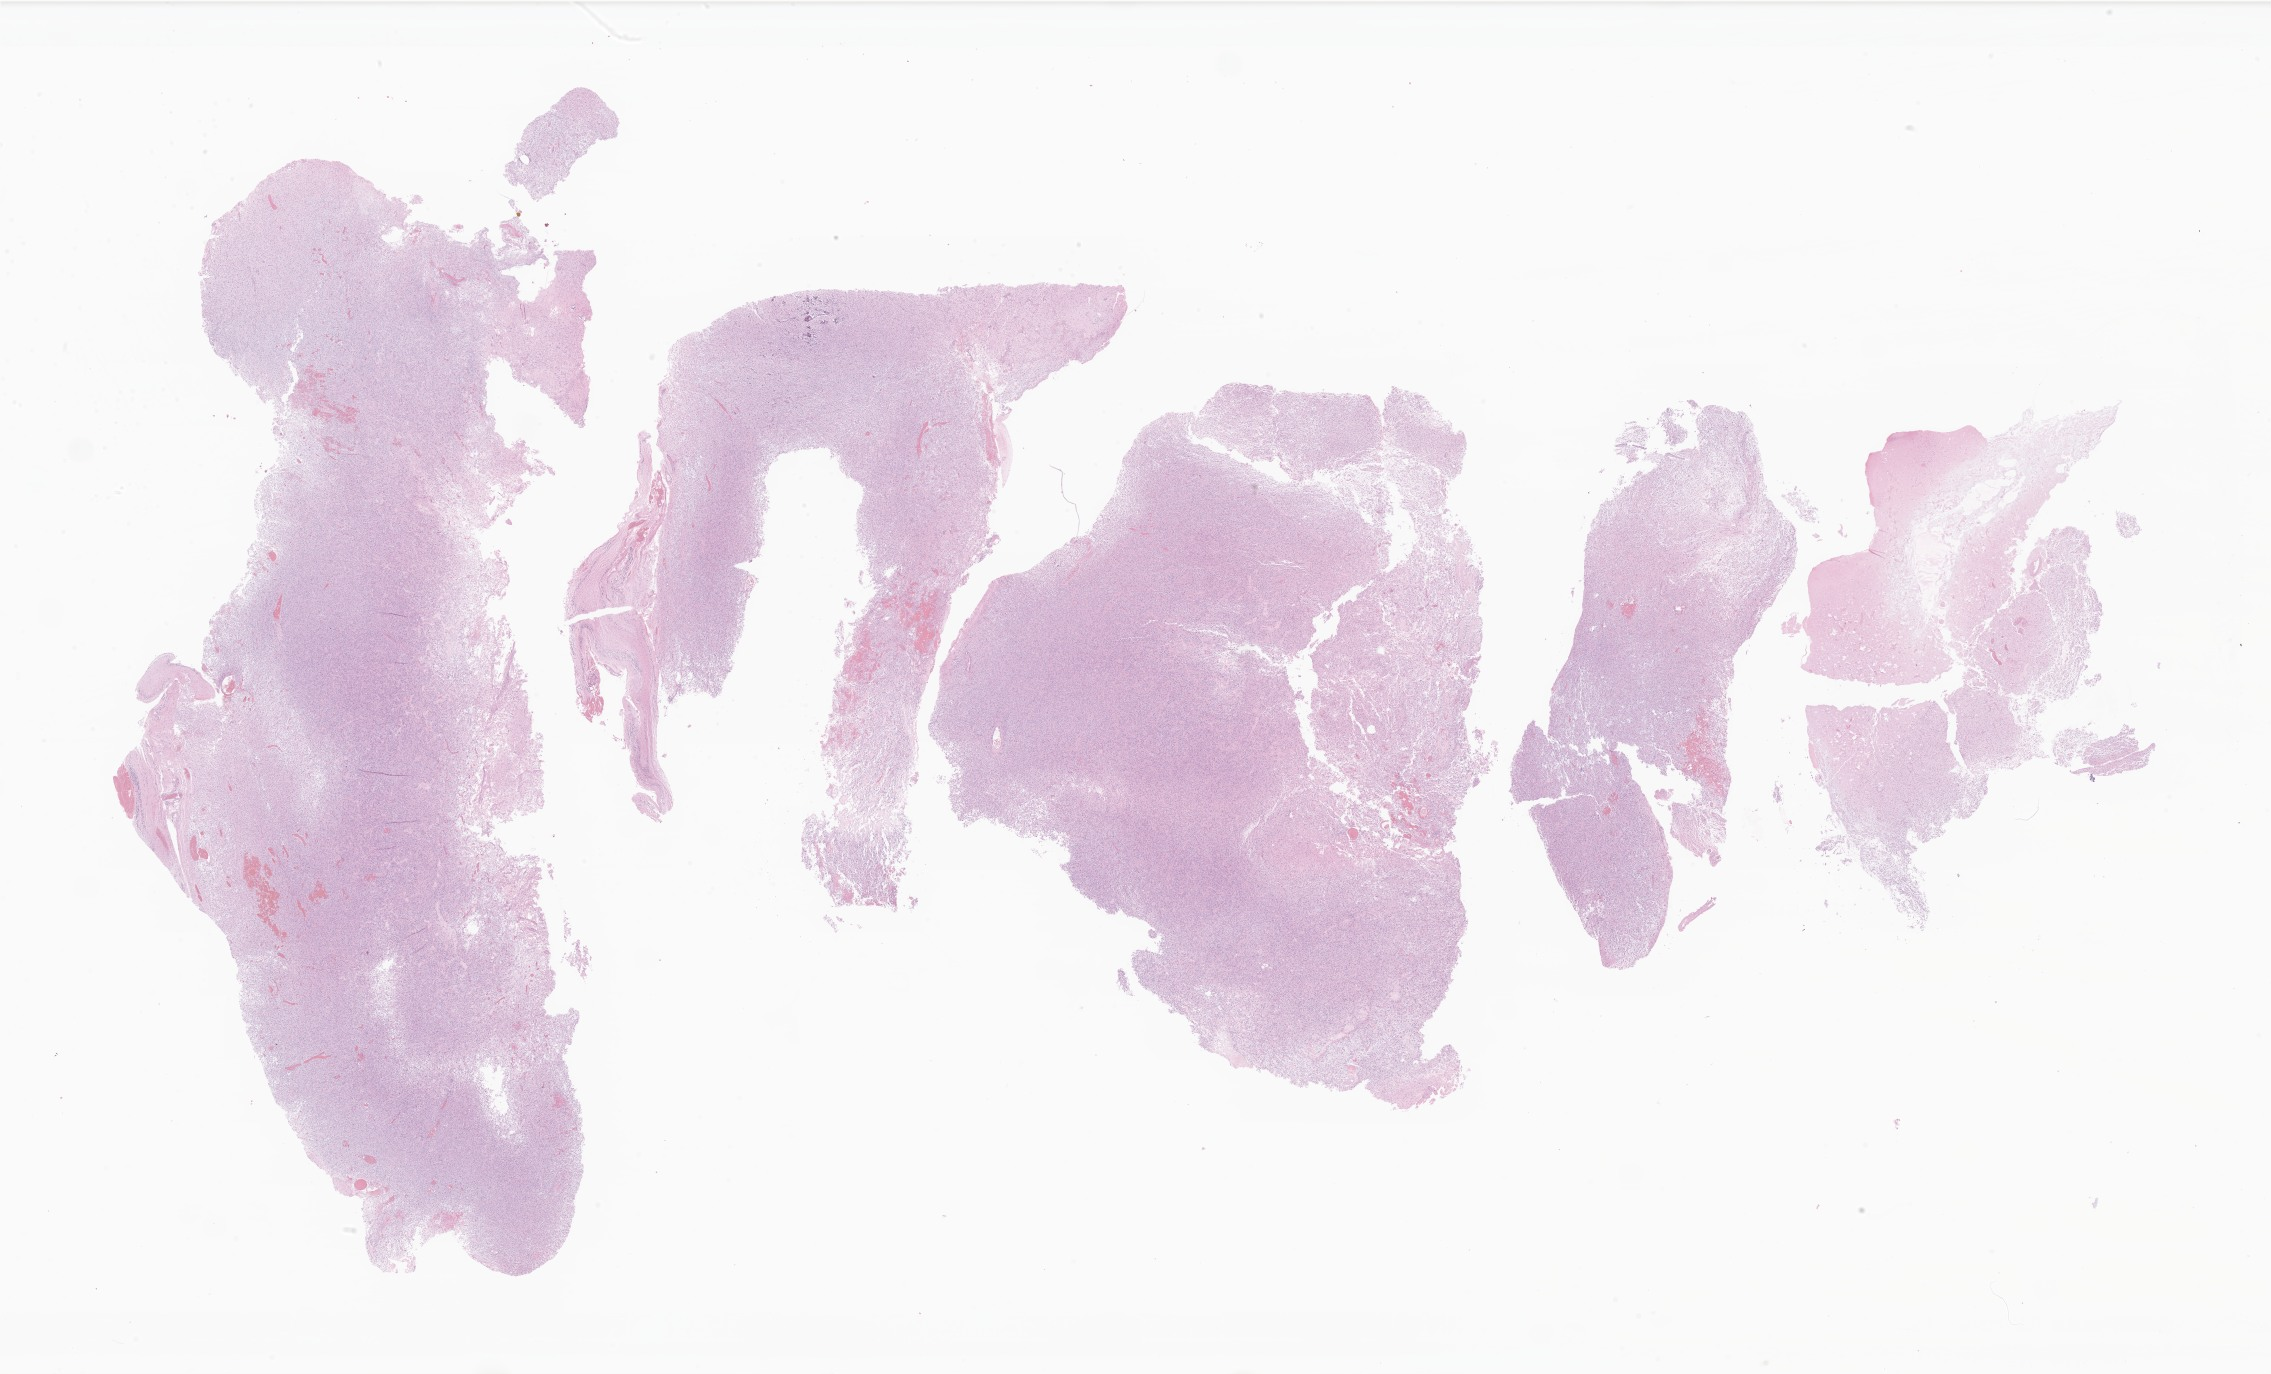
Digitized H&E-stained section of tumor tissue from the brain, shown as a low-resolution overview of the whole scanned area (about 38.3 x 23.2 mm); formalin-fixed paraffin-embedded section. Patient: female, age 147 months (12 years 3 months).
* diagnosis (ICD-O-3 morphology term): Tumor cells, uncertain whether benign or malignant